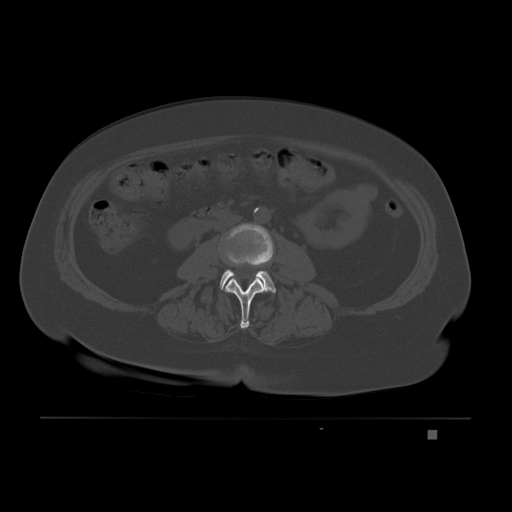
CT including the spine, one axial slice. Position 56 of 221 along the scan axis. Bone window (W 1800 / L 400 HU). 3 mm slice thickness. 512 × 512 image matrix, field of view 474 × 474 mm. Female patient, age 63 years. Case-level facts recorded for this patient, not image findings: primary cancer: breast.
Structures marked on this image (semi-automatically segmented with operator editing):
- L2 vertebra: box from (x=225, y=277) to (x=266, y=328) px
- L3 vertebra: (x=220, y=223)–(x=276, y=293)